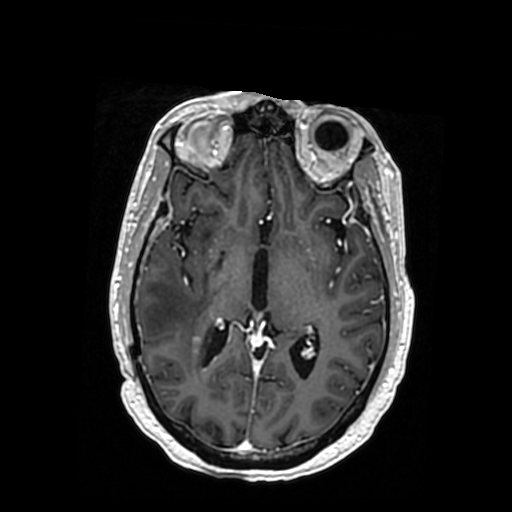
Brain MRI from a brain-tumour surgery series, one axial slice. Slice 190 of 364 in the series (ordered by position). T1-weighted post-contrast. 0.5 mm slice thickness. 512 × 512 image matrix, field of view 260 × 260 mm. Case-level facts recorded for this patient, not image findings: histopathology: Oligodendroglioma; WHO grade: 3; IDH mutation: yes; tumour location: Right Posterior Temporal Inferior Parietal.
Annotated regions visible in this slice (manually delineated by an expert):
- tumour: bounding box <151,337,208,347> (left, top, right, bottom; pixels)